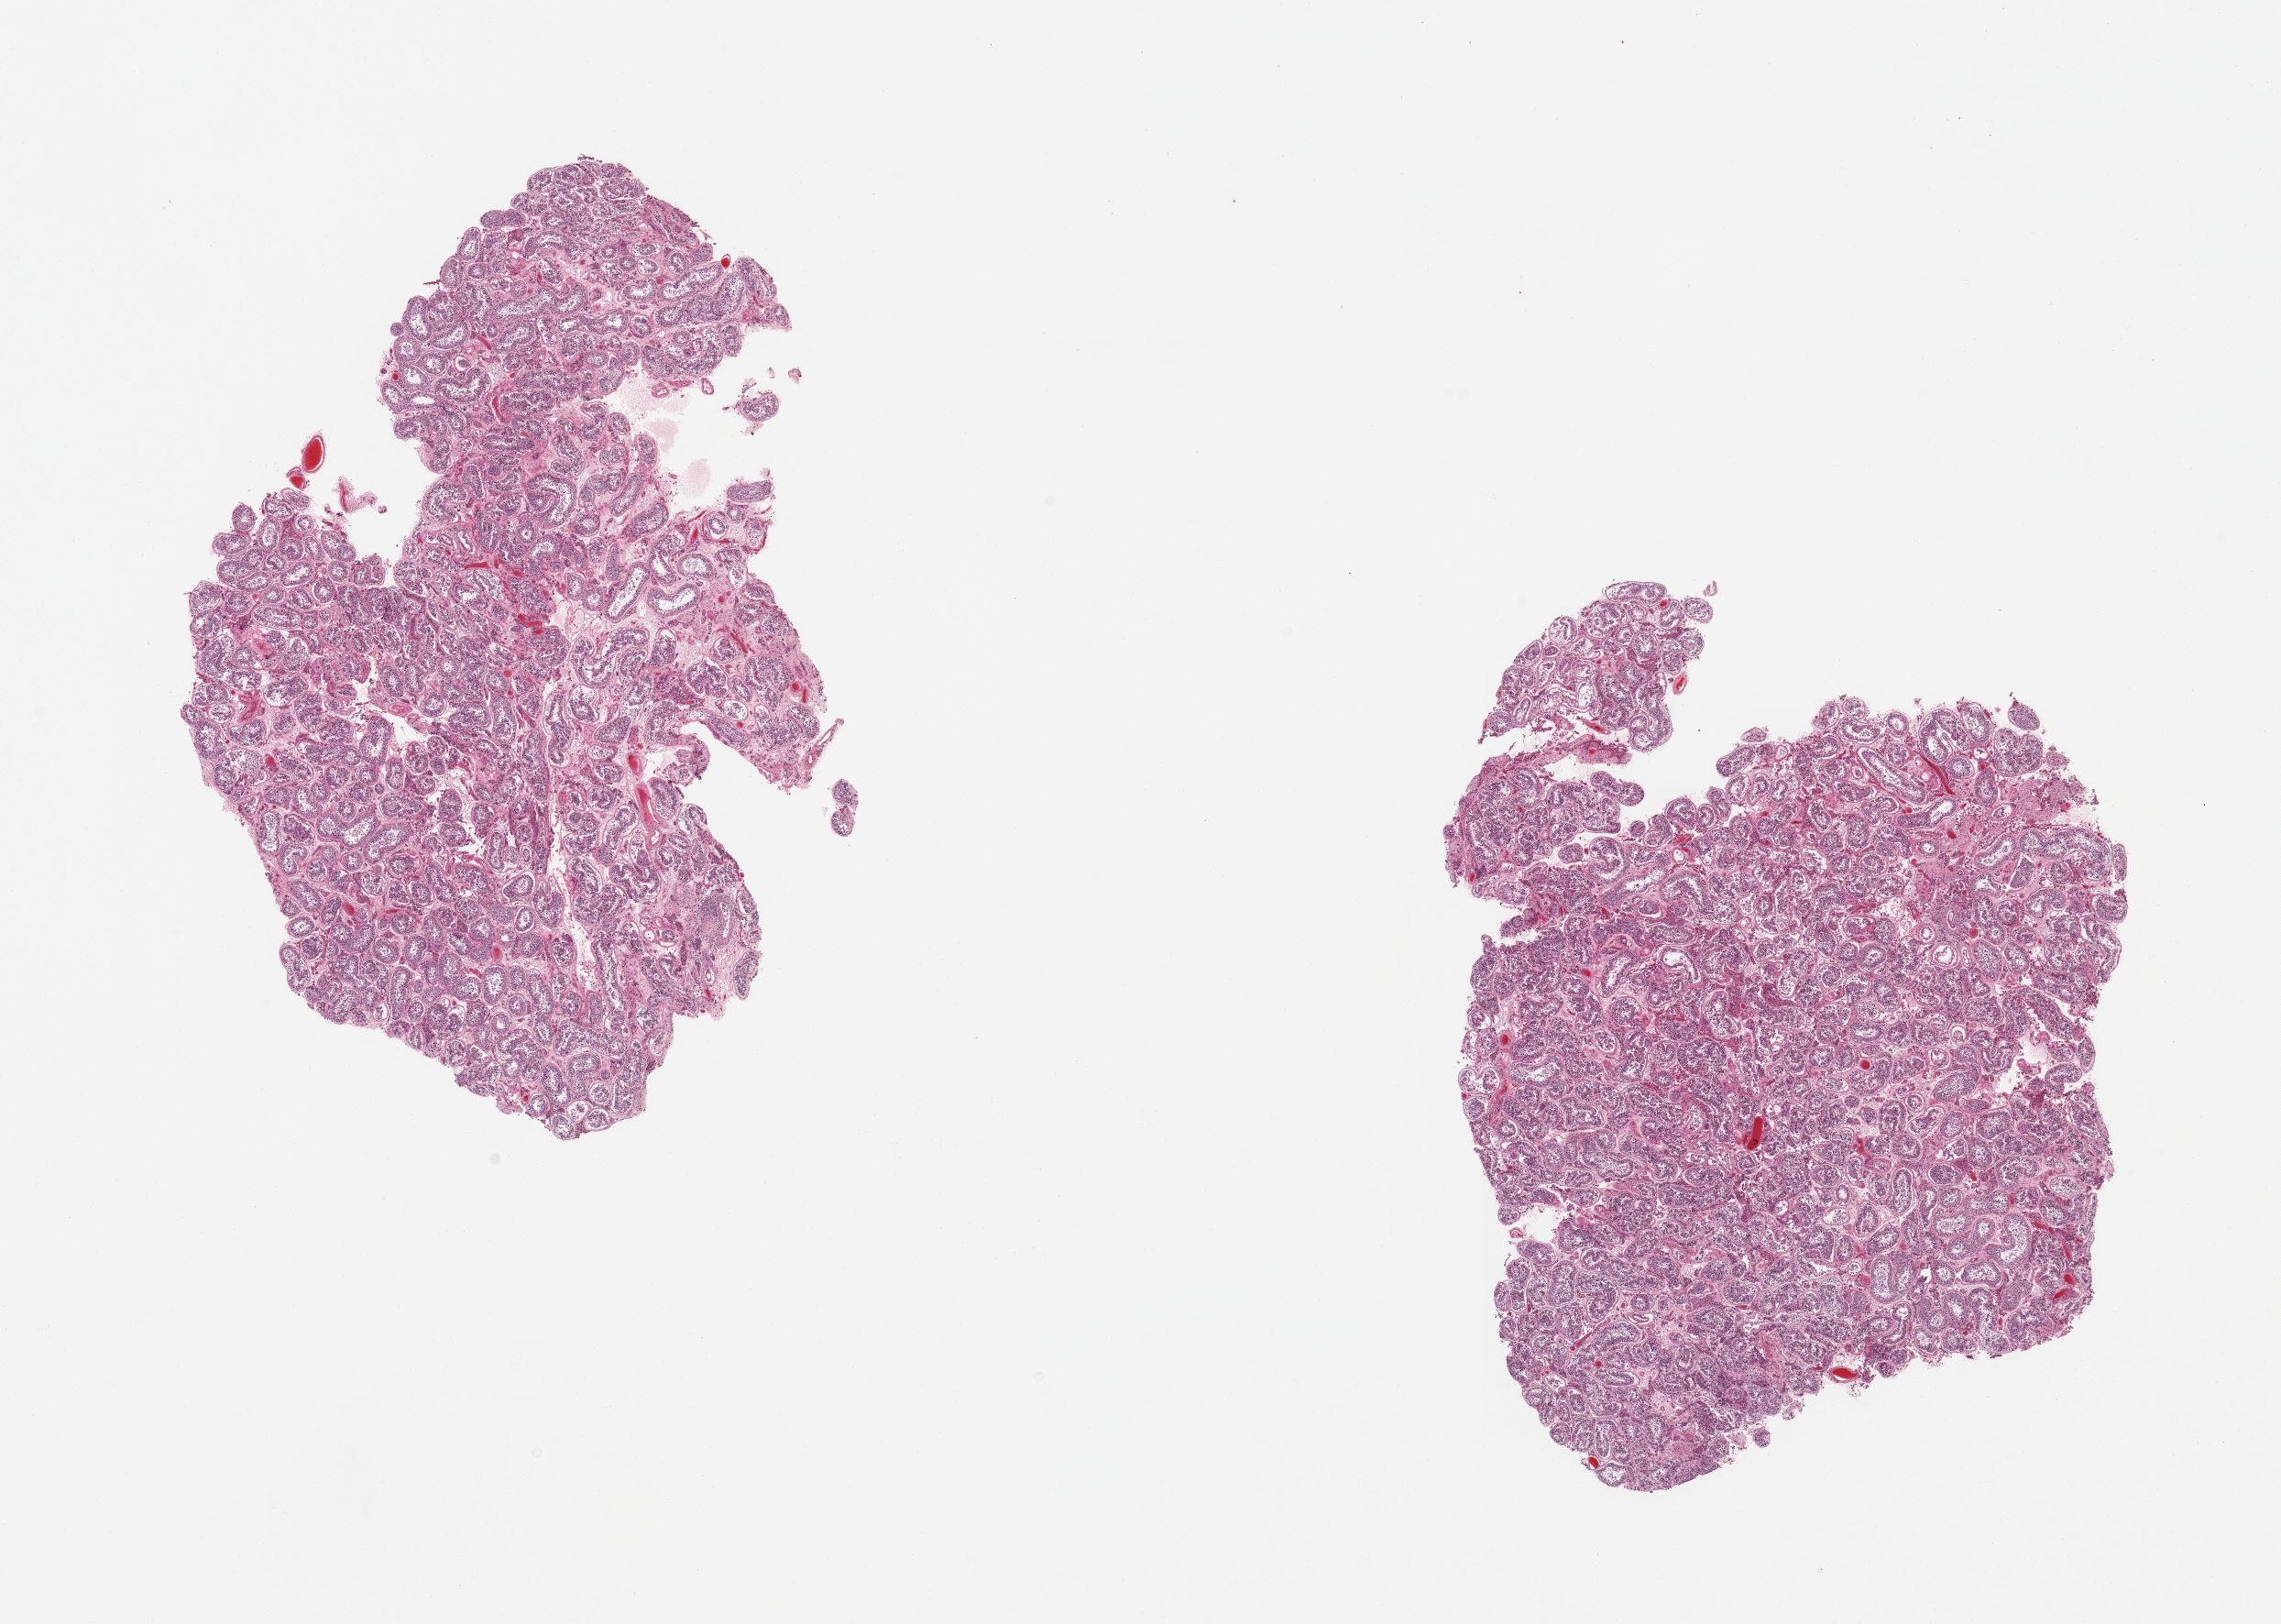
Digitized hematoxylin and eosin (H&E)-stained section, brightfield, a low-resolution overview of the entire scanned area, about 19.7 x 14.0 mm, PAXgene-fixed, paraffin-embedded tissue, target tissue: testis, tissue donor sample.
Reviewer comment on this tissue sample: 2 pieces, spermatogenesis is present.